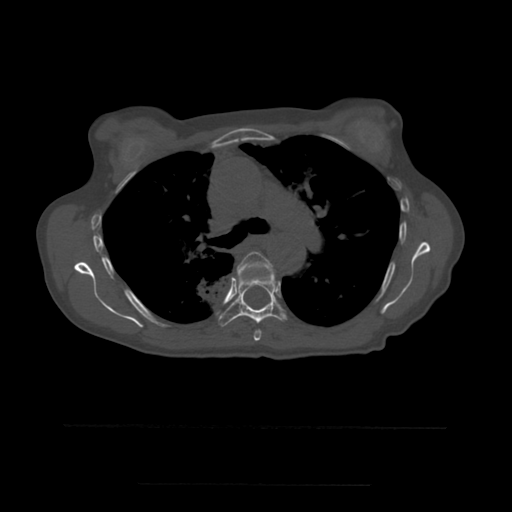
CT including the spine, one axial slice. Slice 380 of 544 in the series (ordered by position). Bone window (W 1800 / L 400 HU). 512 × 512 image matrix, field of view 350 × 350 mm. Patient age 58 years. Case-level facts recorded for this patient, not image findings: primary cancer: lung.
Annotated regions visible in this slice (semi-automatic segmentation, software-assisted and operator-edited):
- T5 vertebra: bounding box <237,252,274,341> (left, top, right, bottom; pixels)
- T6 vertebra: <219,271,288,327>